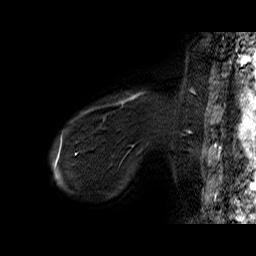
Breast MRI (dynamic contrast-enhanced), one sagittal slice. Slice 6 of 60 in the series (ordered by position). Dynamic contrast-enhanced series, time point 2 of 6 at this slice position (early post-contrast). 1.5 T. TE 6.4 ms, TR 32.9 ms. 256 × 256 image matrix. Female patient. Case-level facts recorded for this patient, not image findings: setting: breast cancer imaged before/during neoadjuvant chemotherapy; receptor status: HER2-positive.
Structures marked on this image (semi-automatic segmentation, software-assisted and operator-edited):
- analysis volume of interest (the breast-tissue region the enhancement analysis was run in; not a lesion): bounding box <71,90,155,146> (left, top, right, bottom; pixels)
- tumour enhancement mask (voxels above the 100 % enhancement threshold inside the analysis volume of interest): <79,92,145,117>